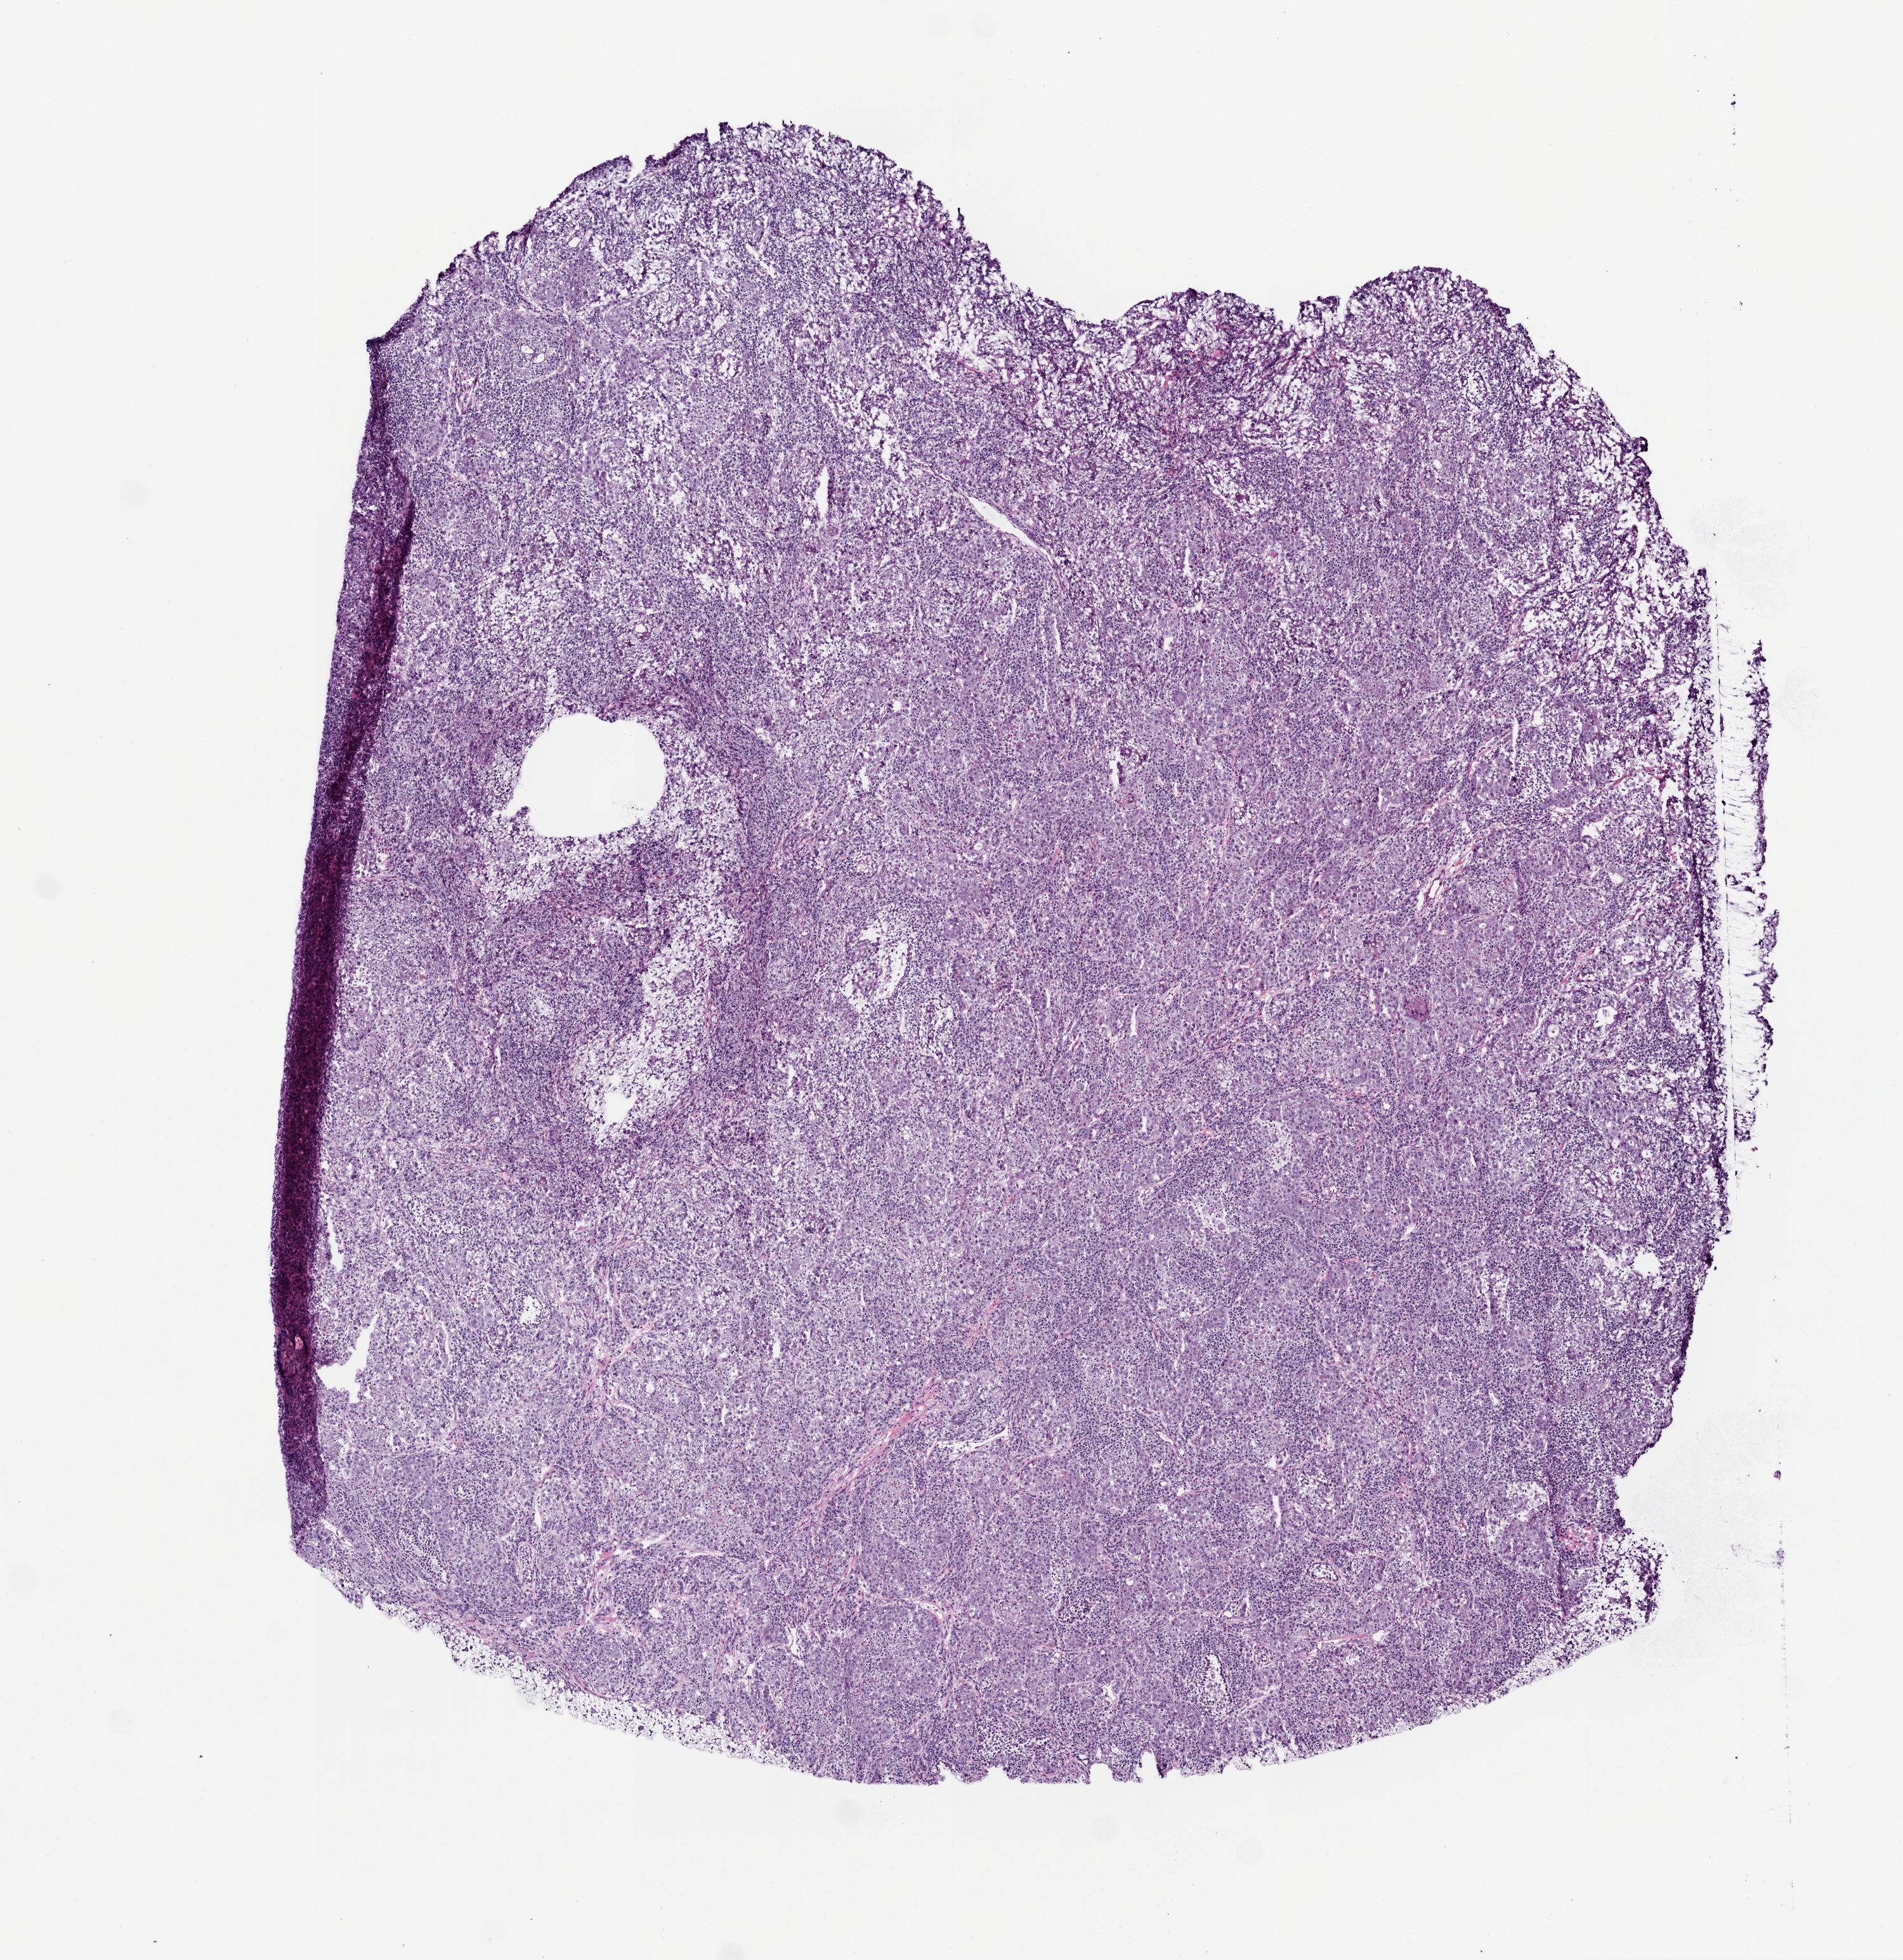
H&E-stained whole-slide image — whole scanned area (about 6.0 x 6.2 mm, acquisition: 20x scan) shown as a low-resolution overview. Frozen section from the top of the tissue portion. Lung, primary tumour sample. Patient: male, age at initial diagnosis 67 years. Pathologist review of this section (percent, as recorded): tumour cells 100%, tumour nuclei 70%, normal cells 0%, stromal cells 0%, necrosis 0%. Inflammatory infiltration, as recorded: lymphocyte infiltration 24%, monocyte infiltration 0%, neutrophil infiltration 0%.
AJCC pathologic stage: IIIA (6th edition). Laterality: left. Diagnosis: Adenocarcinoma, NOS.